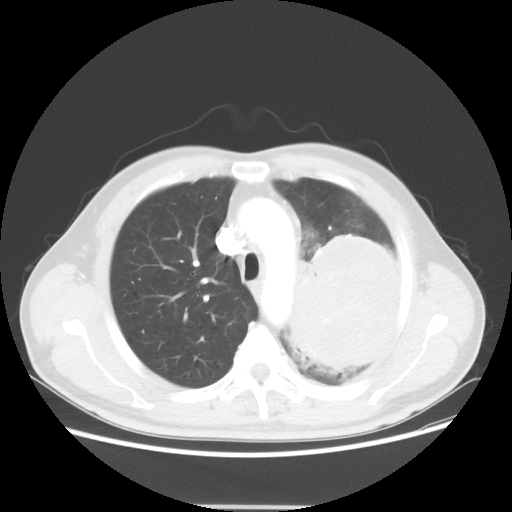
Chest CT, one axial slice; position 40 of 53 along the scan axis; reconstruction kernel STANDARD; lung window (W 1500 / L -600 HU); 5 mm slice thickness; 512 × 512 image matrix. Male patient, age 60 years. From the clinical record (not read from this slice): clinical TNM (as recorded): T4 N1 M1a.
Structures marked on this image (rectangle marked by the reading radiologist):
- lung tumour (recorded histology: large cell carcinoma): box from (x=283, y=222) to (x=401, y=389) px